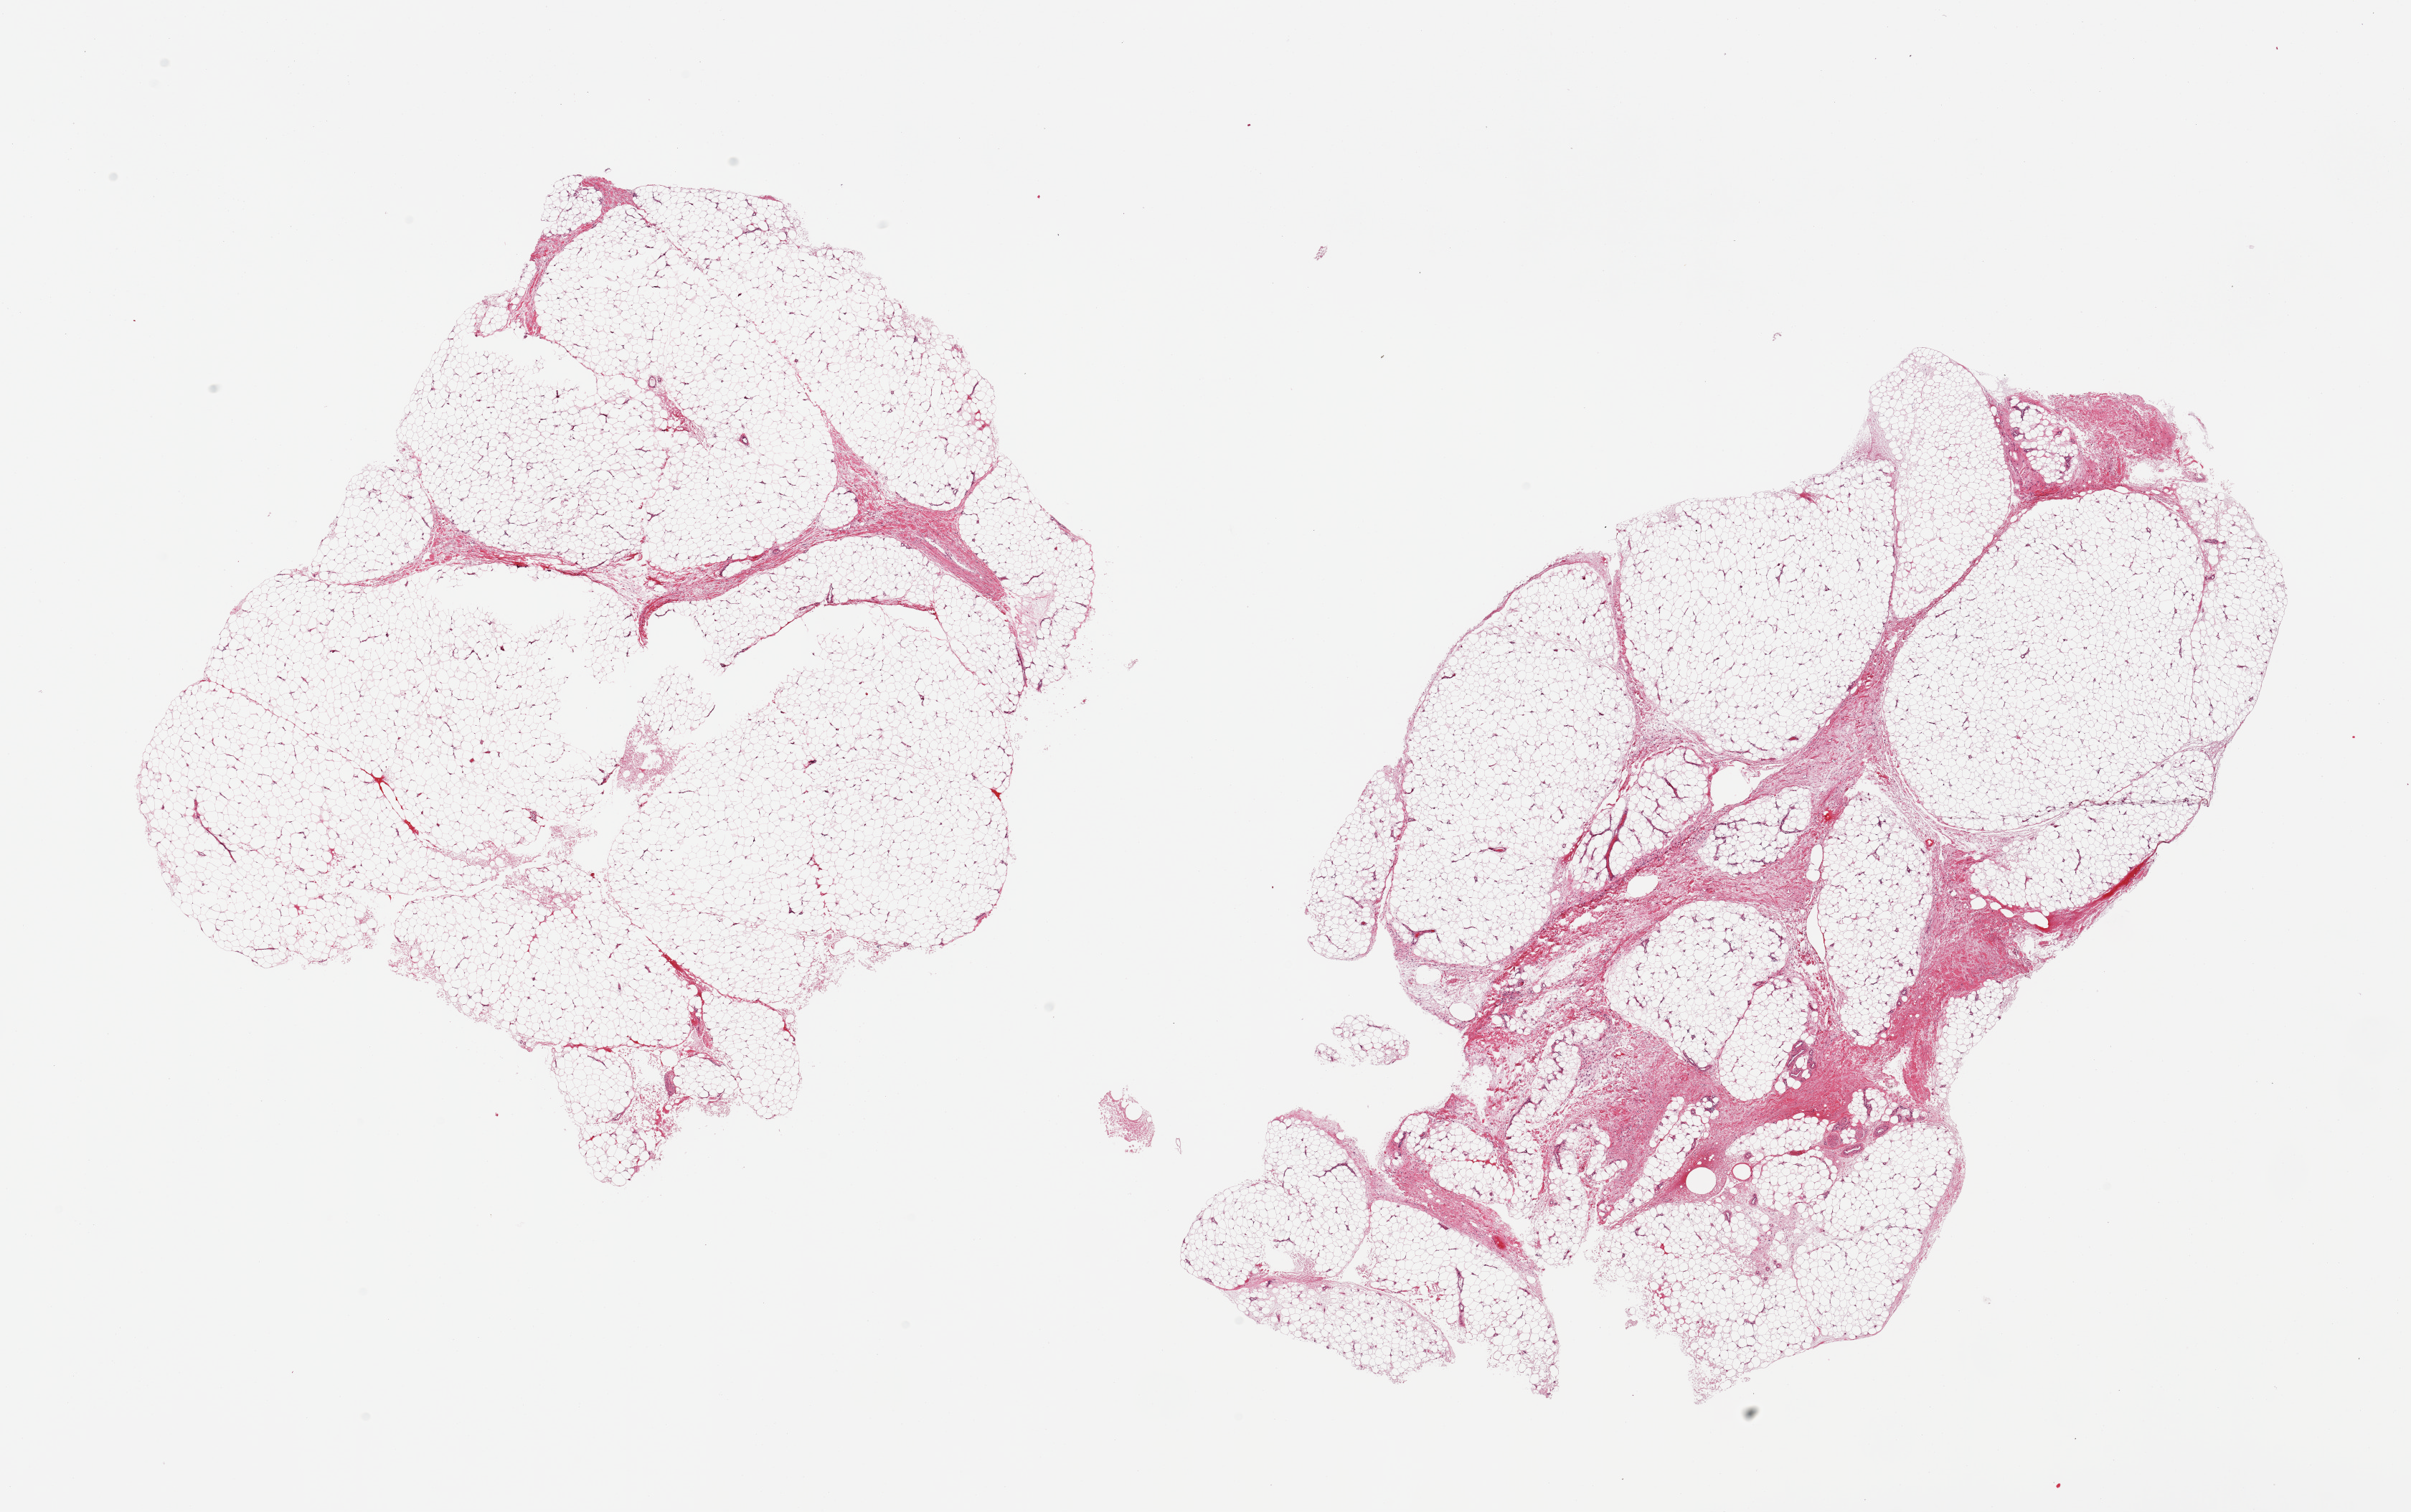
Digitized haematoxylin and eosin-stained section, whole scanned area (about 26.6 x 16.7 mm, acquisition: 20x scan) shown as a low-resolution overview, PAXgene-fixed paraffin-embedded (PFPE) section, target tissue: adipose tissue, donor tissue sample. Donor sex: male.
Review note (as recorded): 2 pieces; 5 & 10% fibrous stroma content.